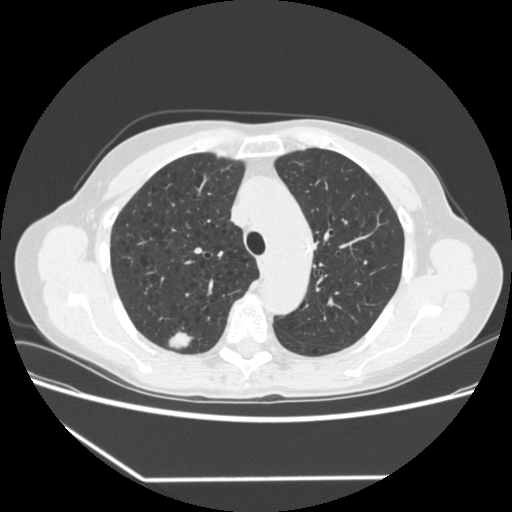
Low-dose screening chest CT, one axial slice. Slice 246 of 323 in the series (ordered by position). Reconstruction kernel STANDARD. Lung window (W 1500 / L -600 HU). 512 × 512 image matrix, field of view 360 × 360 mm.
Annotated regions visible in this slice (outlined manually by an expert reader):
- lesion 1 (tumor, upper lobe of right lung): bounding box [x1, y1, x2, y2] px = [169, 328, 192, 349]